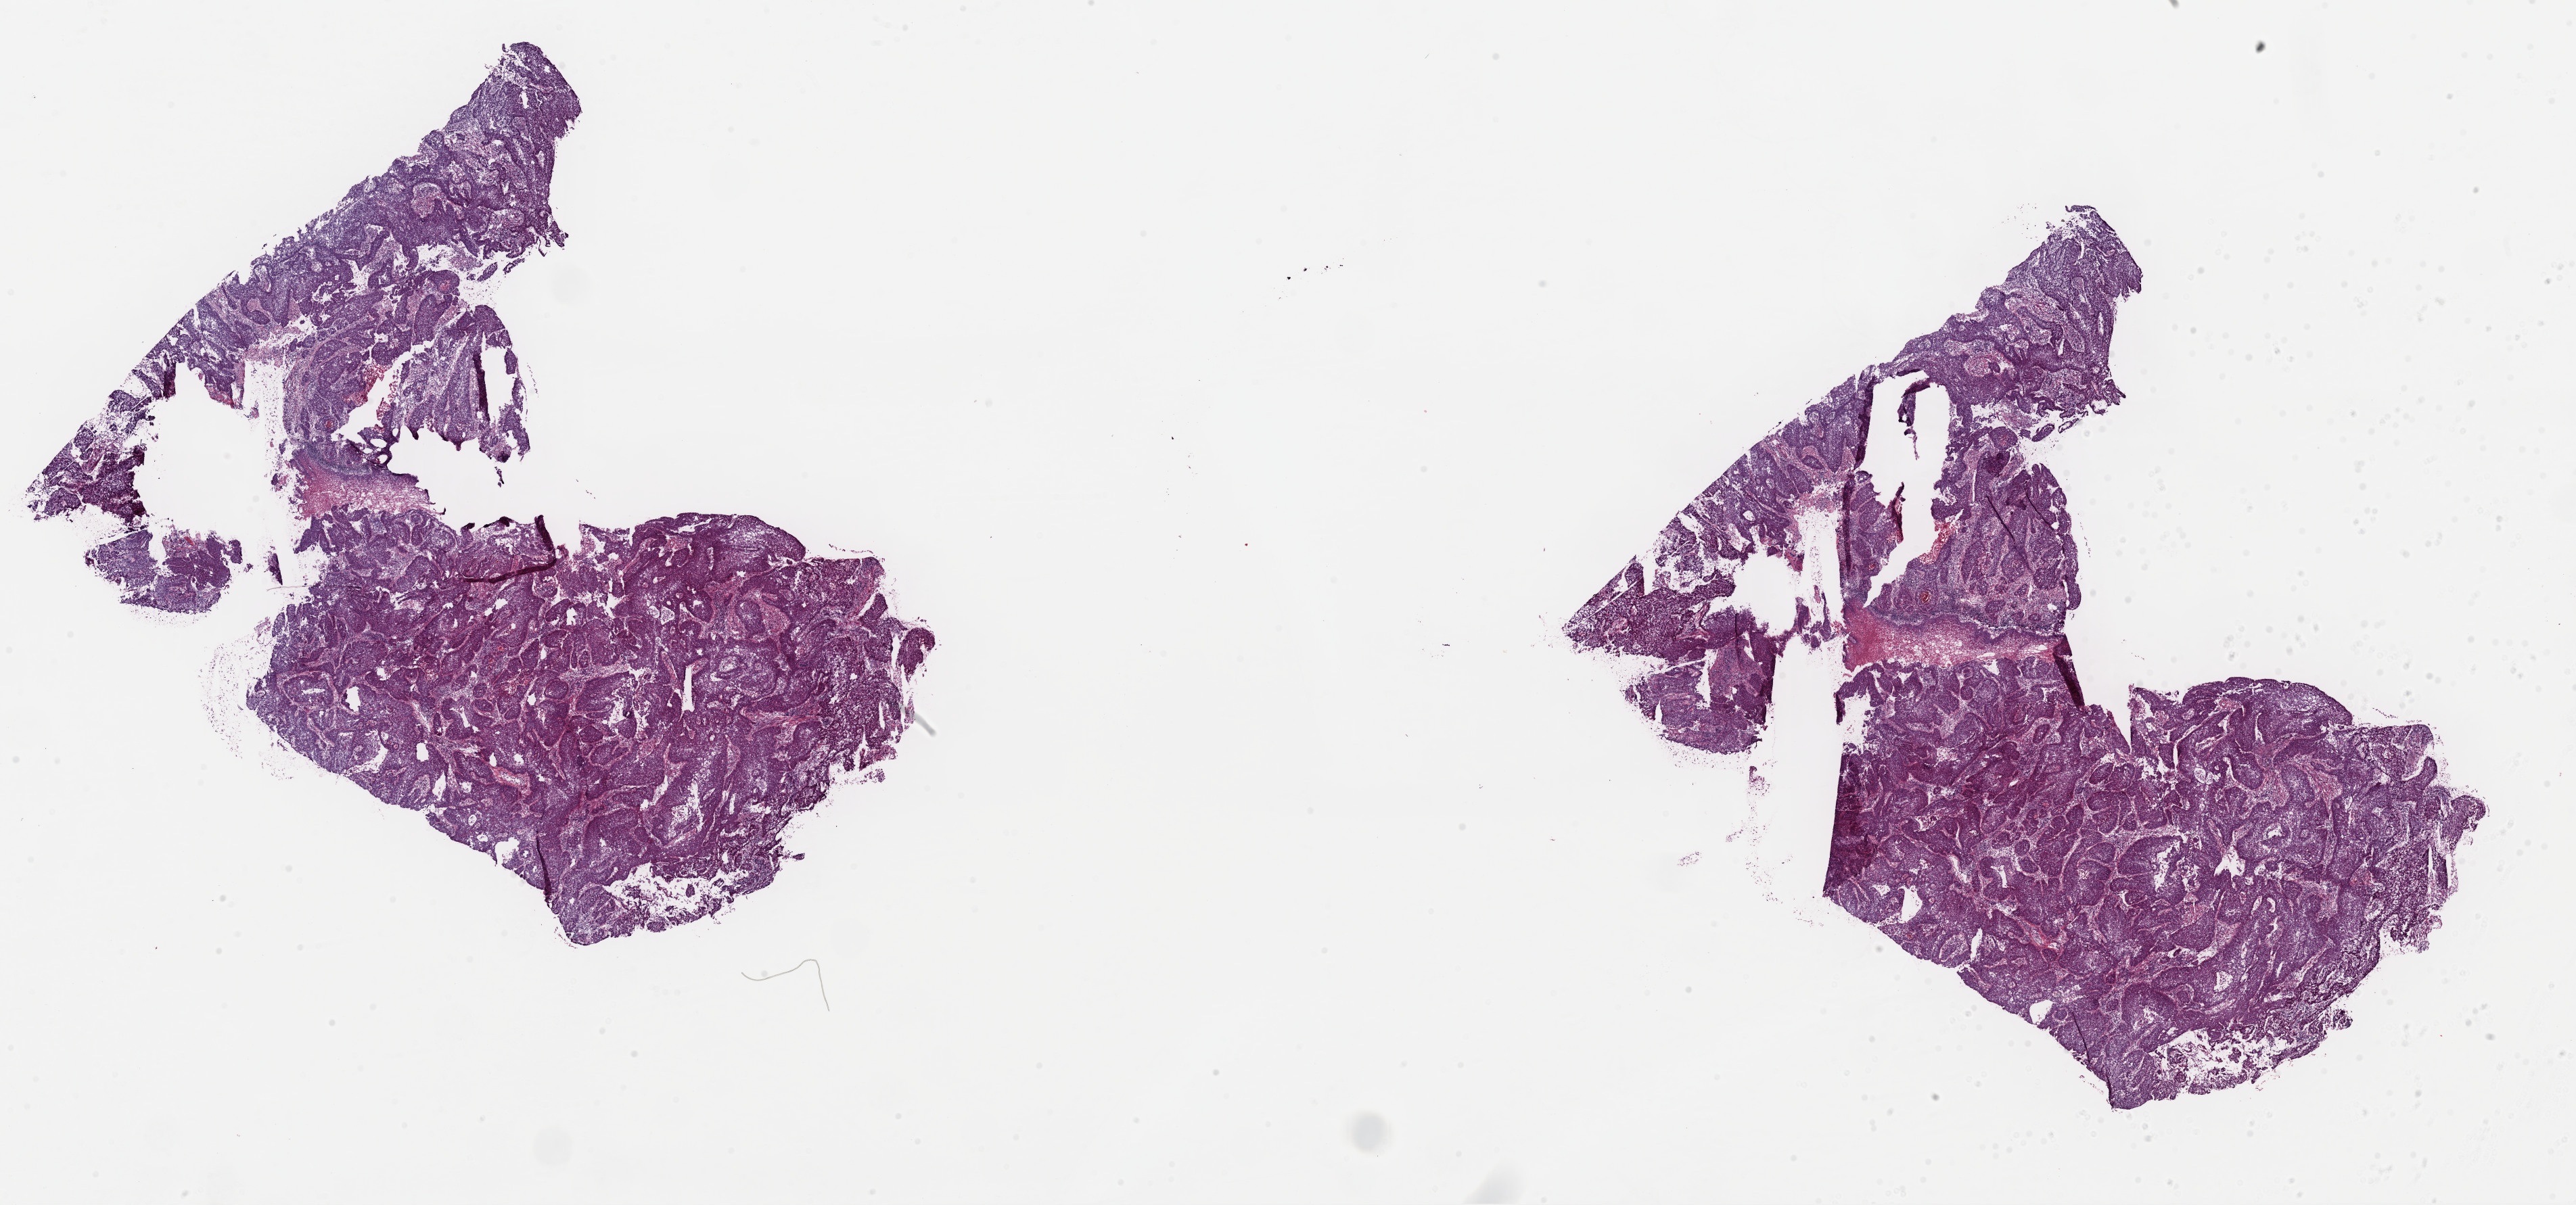
Digitized Hematoxylin and eosin (H&E) stained tissue section (whole slide), whole scanned area (about 30.1 x 14.1 mm) shown as a low-resolution overview. Frozen section. Primary tumour sample from the cervix. Female, age 36 years at initial diagnosis. Composition of this section per pathologist review: tumour cells 80%, tumour nuclei 80%, normal cells 7%, stromal cells 12%, necrosis 1%. Infiltration values recorded for this section: lymphocyte infiltration 10%, monocyte infiltration 0%, neutrophil infiltration 0%.
Diagnosis: Squamous cell carcinoma, large cell, nonkeratinizing, NOS (cervix uteri). FIGO stage: IIIB.